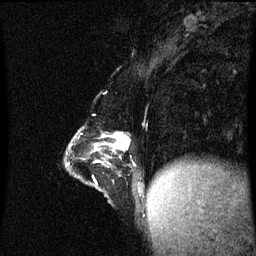
Breast MRI (dynamic contrast-enhanced), one sagittal slice. Position 21 of 60 along the scan axis. Dynamic contrast-enhanced series, image 2 of 3 at this slice position (ordered by acquisition). 1.5 T. TE 4.2 ms, TR 8.9 ms. 256 × 256 image matrix, field of view 200 × 200 mm. Female patient, age 47 years. Case-level facts recorded for this patient, not image findings: setting: breast cancer imaged before/during neoadjuvant chemotherapy; receptor status: HR-positive, HER2-negative.
Structures marked on this image (semi-automatic segmentation, software-assisted and operator-edited):
- analysis volume of interest (the breast-tissue region the enhancement analysis was run in; not a lesion): box from (x=67, y=122) to (x=148, y=209) px
- tumour enhancement mask (voxels above the 70 % enhancement threshold inside the analysis volume of interest): (x=113, y=134)–(x=130, y=149)